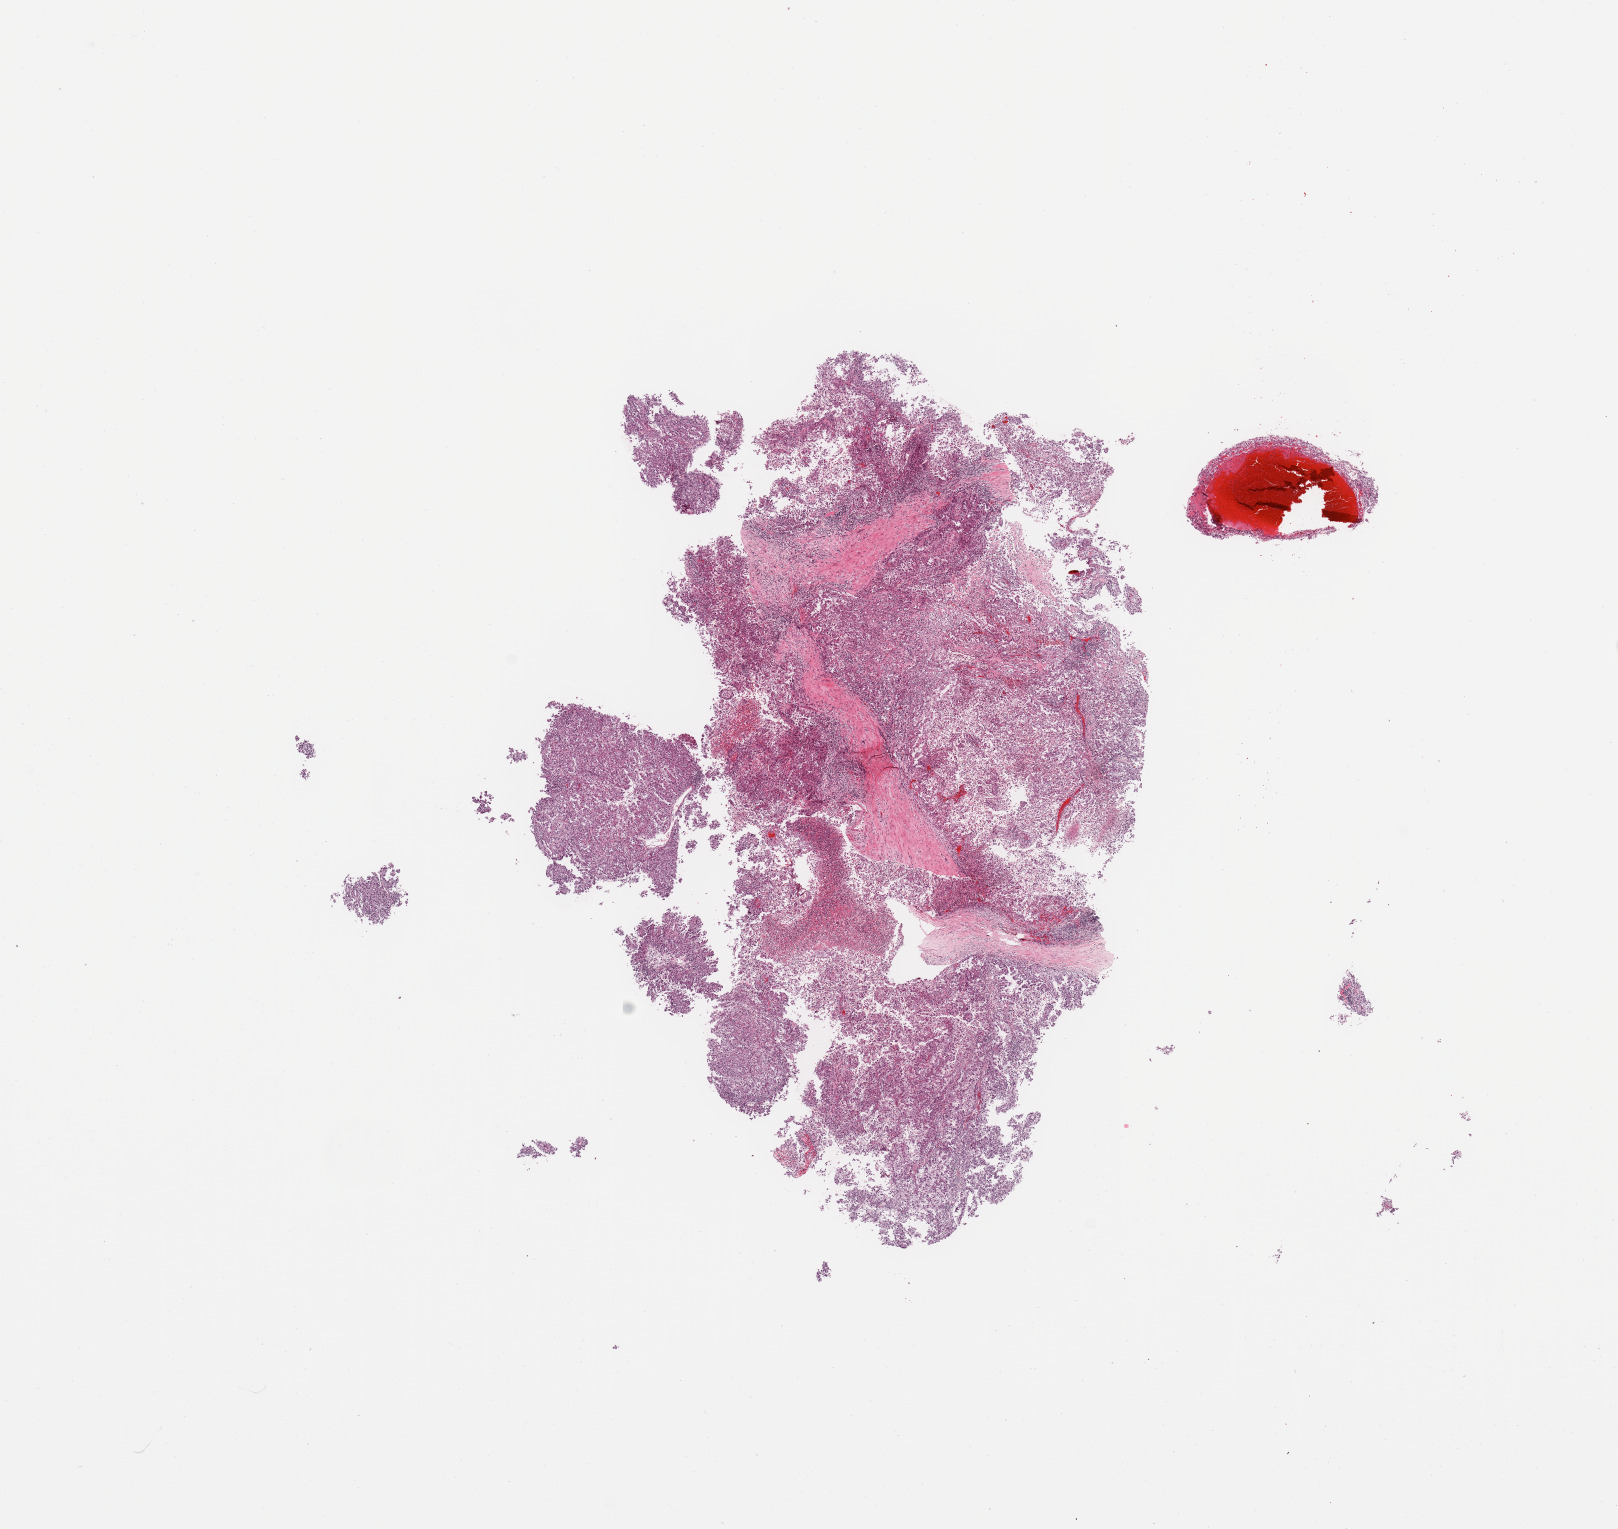
H&E-stained whole-slide image — a low-resolution overview of the entire scanned area, about 12.8 x 12.1 mm. Kidney, tumour tissue. 50-year-old male patient. Histologic grade: G2 (moderately differentiated).
* AJCC pathologic stage: III
* diagnosis: Renal cell carcinoma, NOS